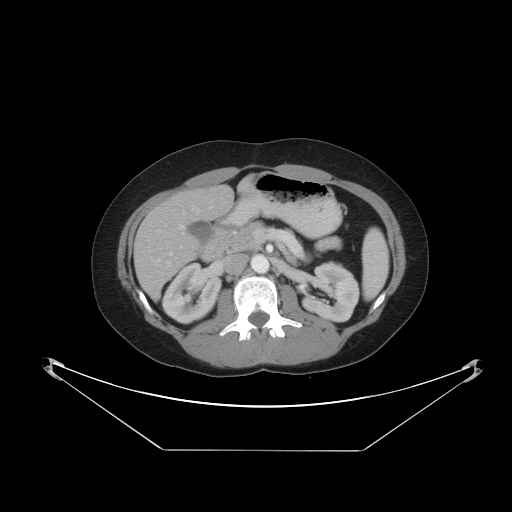
Contrast-enhanced abdominal CT, one axial slice. Slice 21 of 48 in the series (ordered by position). 120 kVp. Intravenous contrast given. Soft-tissue window (W 400 / L 40 HU). 5 mm slice thickness. 512 × 512 image matrix. Female patient, age 38 years. Case-level facts recorded for this patient, not image findings: diagnosis: colorectal cancer liver metastases, imaged before liver resection; multiple liver metastases: yes; largest metastasis: 2.5 cm.
Structures marked on this image (expert manual segmentation):
- hepatic veins: bounding box <179,208,197,229> (left, top, right, bottom; pixels)
- liver: <135,180,254,296>
- planned liver remnant (the part of the liver to remain after resection): <169,180,255,221>
- portal vein (with intrahepatic branches): <158,207,212,266>